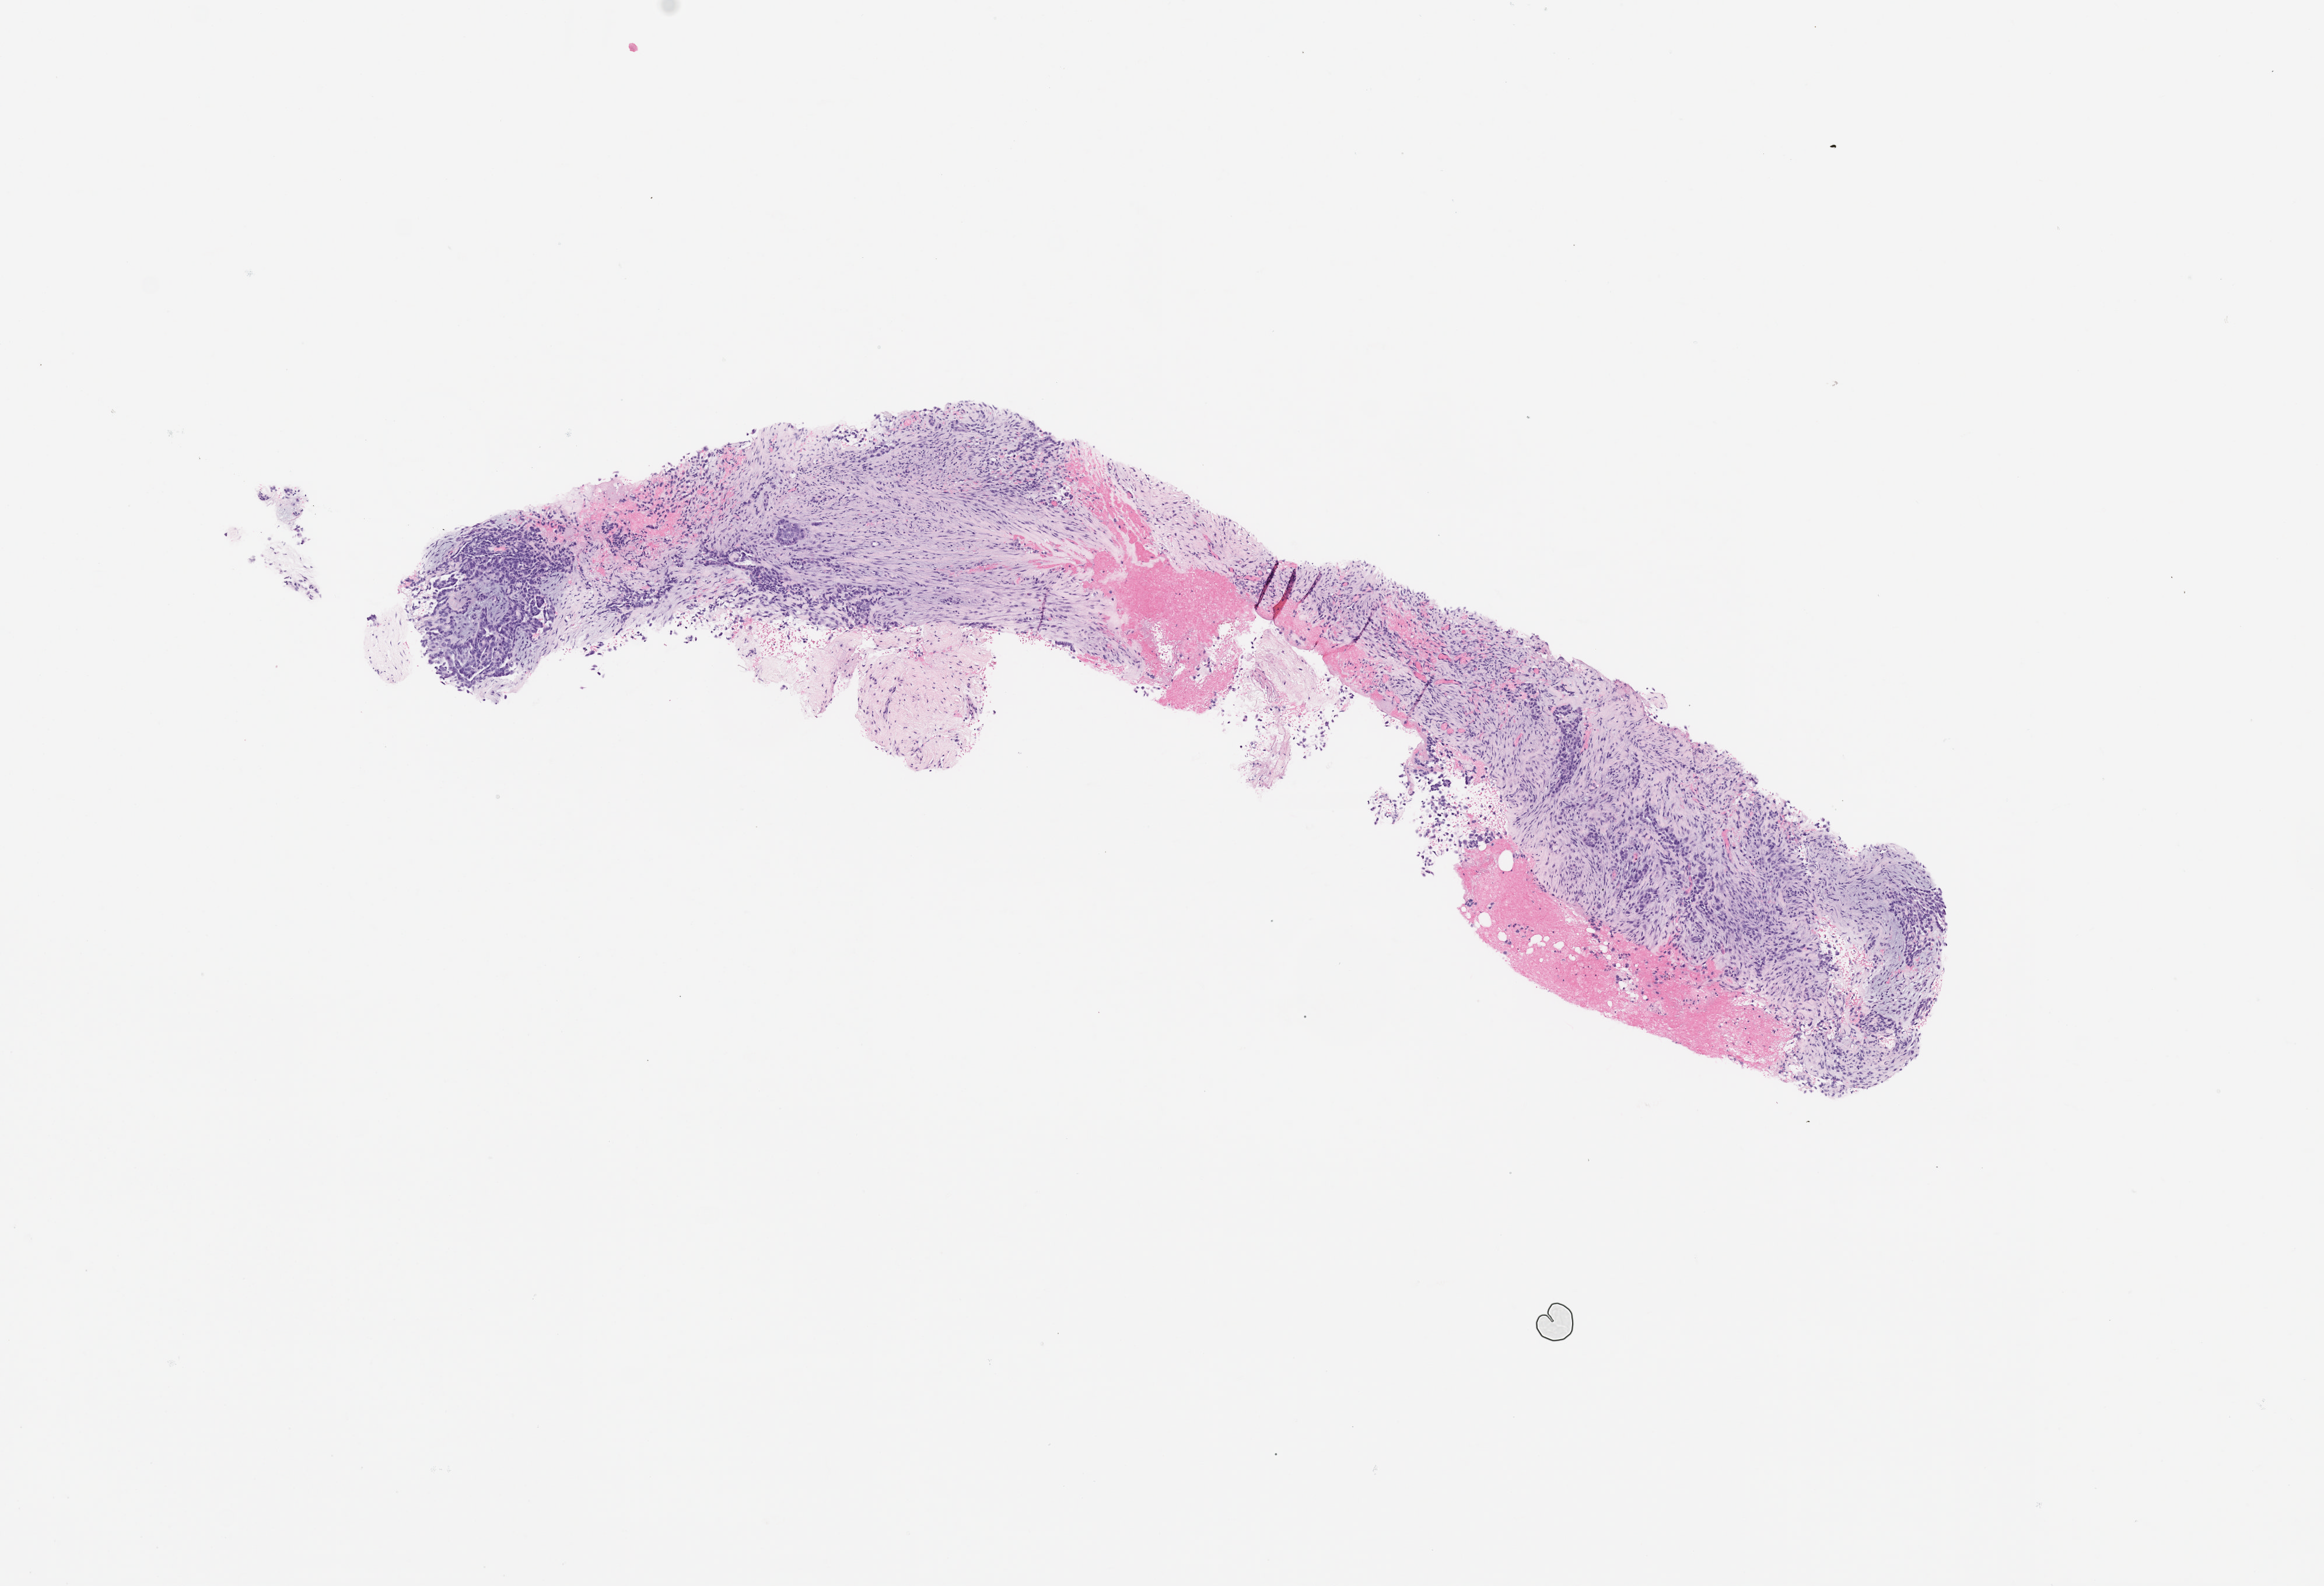
Haematoxylin and eosin whole-slide image of the patient's (originator) tumor tissue — a low-resolution overview of the entire scanned area, about 8.0 x 5.5 mm; formalin-fixed paraffin-embedded section. Patient male; aged 67.
• diagnosis: Mesothelial Neoplasm